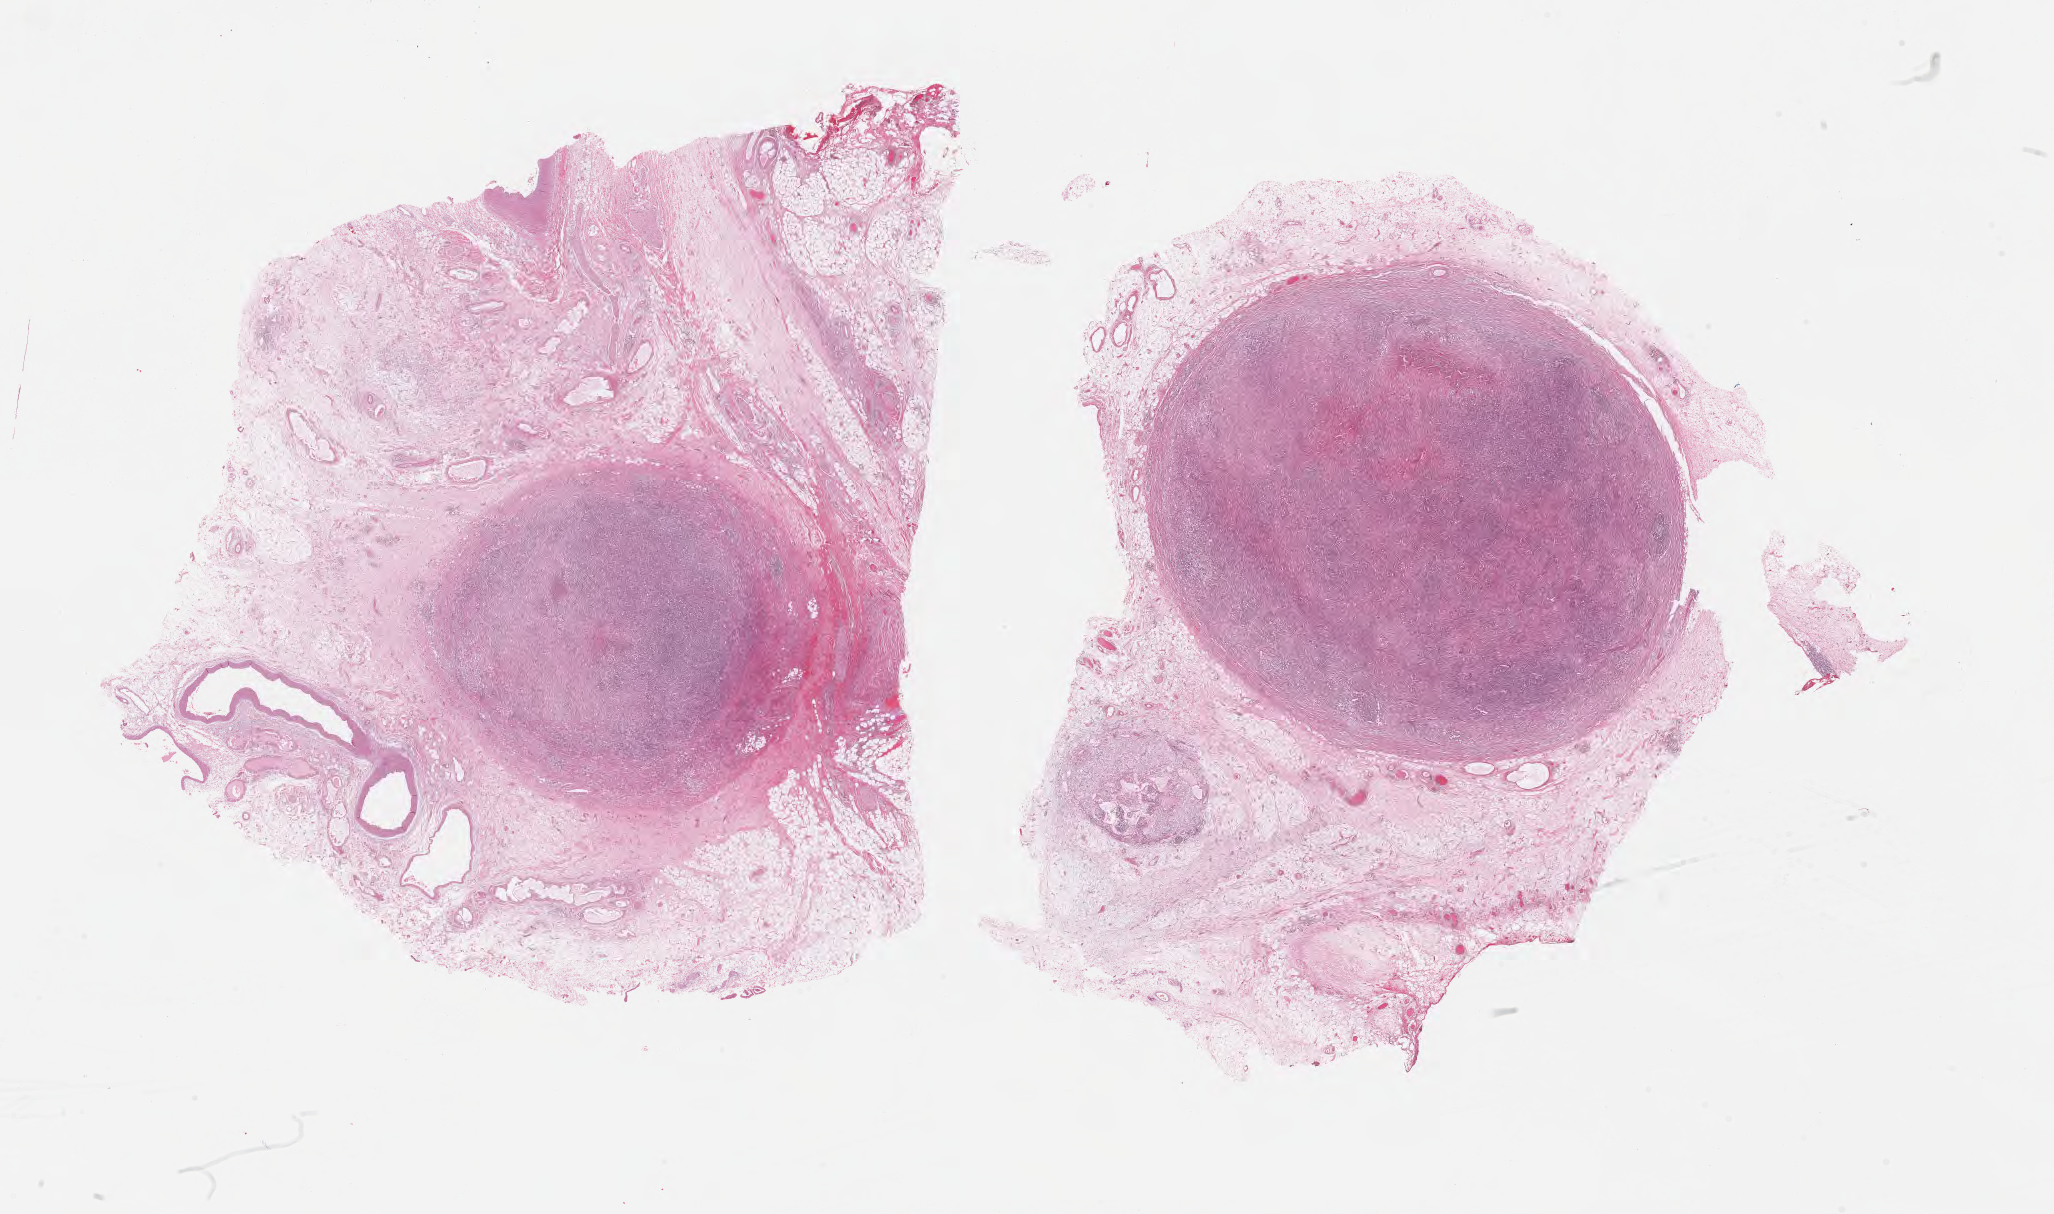
Whole-slide image, hematoxylin and eosin (H&E) stain — low-resolution overview of the scanned area, about 33.2 x 19.6 mm, formalin-fixed, paraffin-embedded (FFPE) tissue, specimen: primary tumor. Patient: female, age 44 years. Slide review estimates, as recorded: tumor cells 60%, tumor nuclei 70%, stromal cells 10%, necrosis 10%, normal cells 20%. Inflammatory infiltration, as recorded: lymphocyte infiltration 70%, monocyte infiltration 15%, neutrophil infiltration 5%.
Histologic diagnosis: Burkitt lymphoma, NOS. Section: top of the tissue portion.